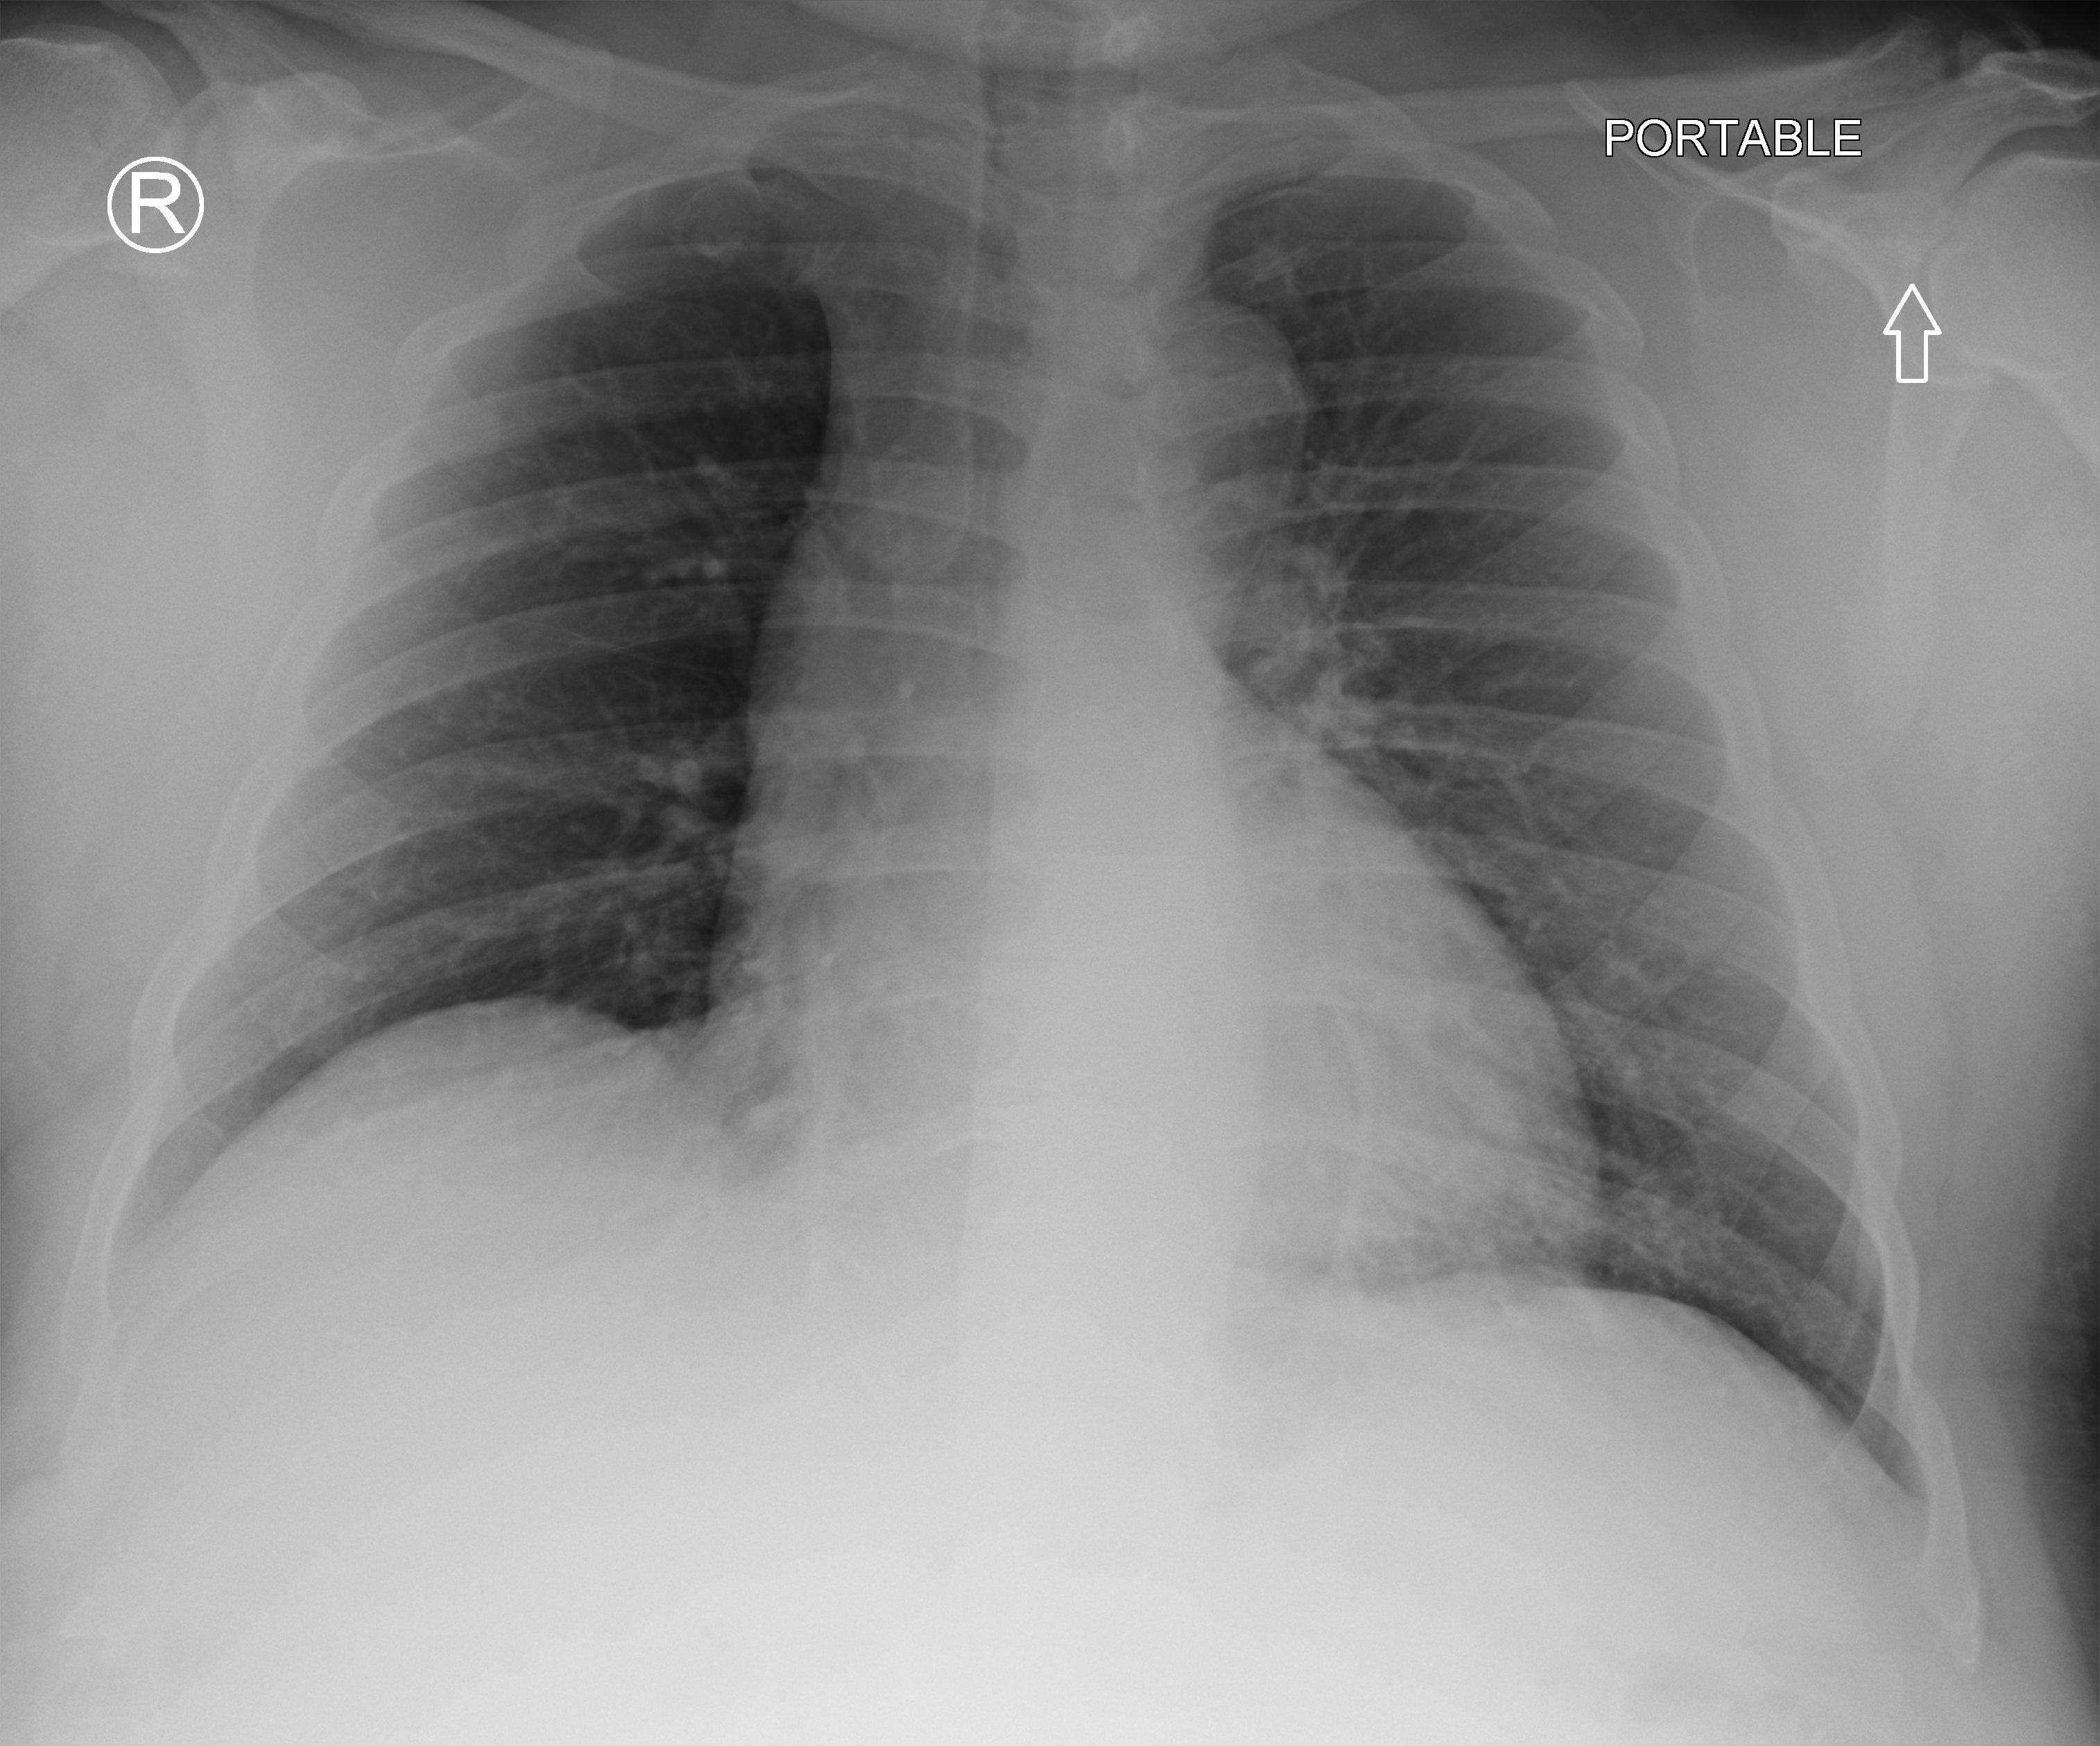
Bedside chest radiograph (computed radiography). Male patient hospitalised with COVID-19, age 18–59 years.
Hospital-stay facts (about this admission, not read from this image; timing relative to this image not recorded):
- hypertension (admission record): no
- length of hospital stay: 2 days
- mechanically ventilated during this hospital stay: no